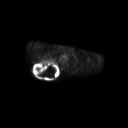
FDG PET of an extremity soft-tissue mass (from a PET/CT study), one axial slice. Position 206 of 267 along the scan axis. 3.27 mm slice thickness. 128 × 128 image matrix. Male patient, age 61 years. From the clinical record (not read from this slice): histological type: pleiomorphic spindle cell undifferentiated; grade: high; site of the primary tumour: right parascapusular.
Structures marked on this image (expert contour drawn on MRI and transferred to this co-registered scan by the dataset authors):
- gross tumour volume including surrounding oedema: bounding box [x1, y1, x2, y2] px = [33, 61, 60, 77]
- gross tumour volume (mass): [33, 61, 59, 77]